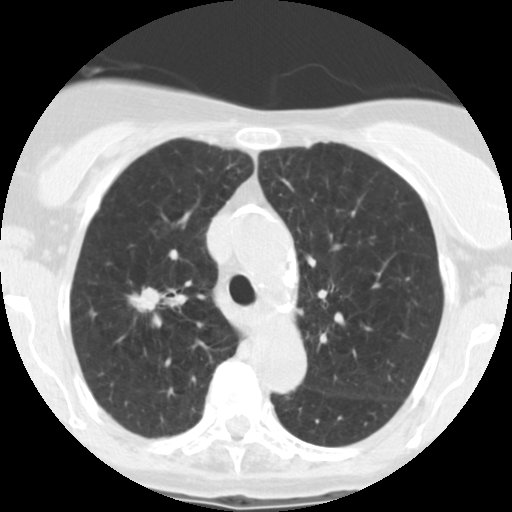
Low-dose screening chest CT, one axial slice. Position 178 of 246 along the scan axis. Reconstruction kernel STANDARD. 120 kVp. Lung window (W 1500 / L -600 HU). 2.5 mm slice thickness. 512 × 512 image matrix, field of view 288 × 288 mm.
Outlined on this slice (outlined manually by an expert reader):
- lesion 1 (tumor, upper lobe of right lung): bounding box [x1, y1, x2, y2] px = [128, 287, 162, 313]